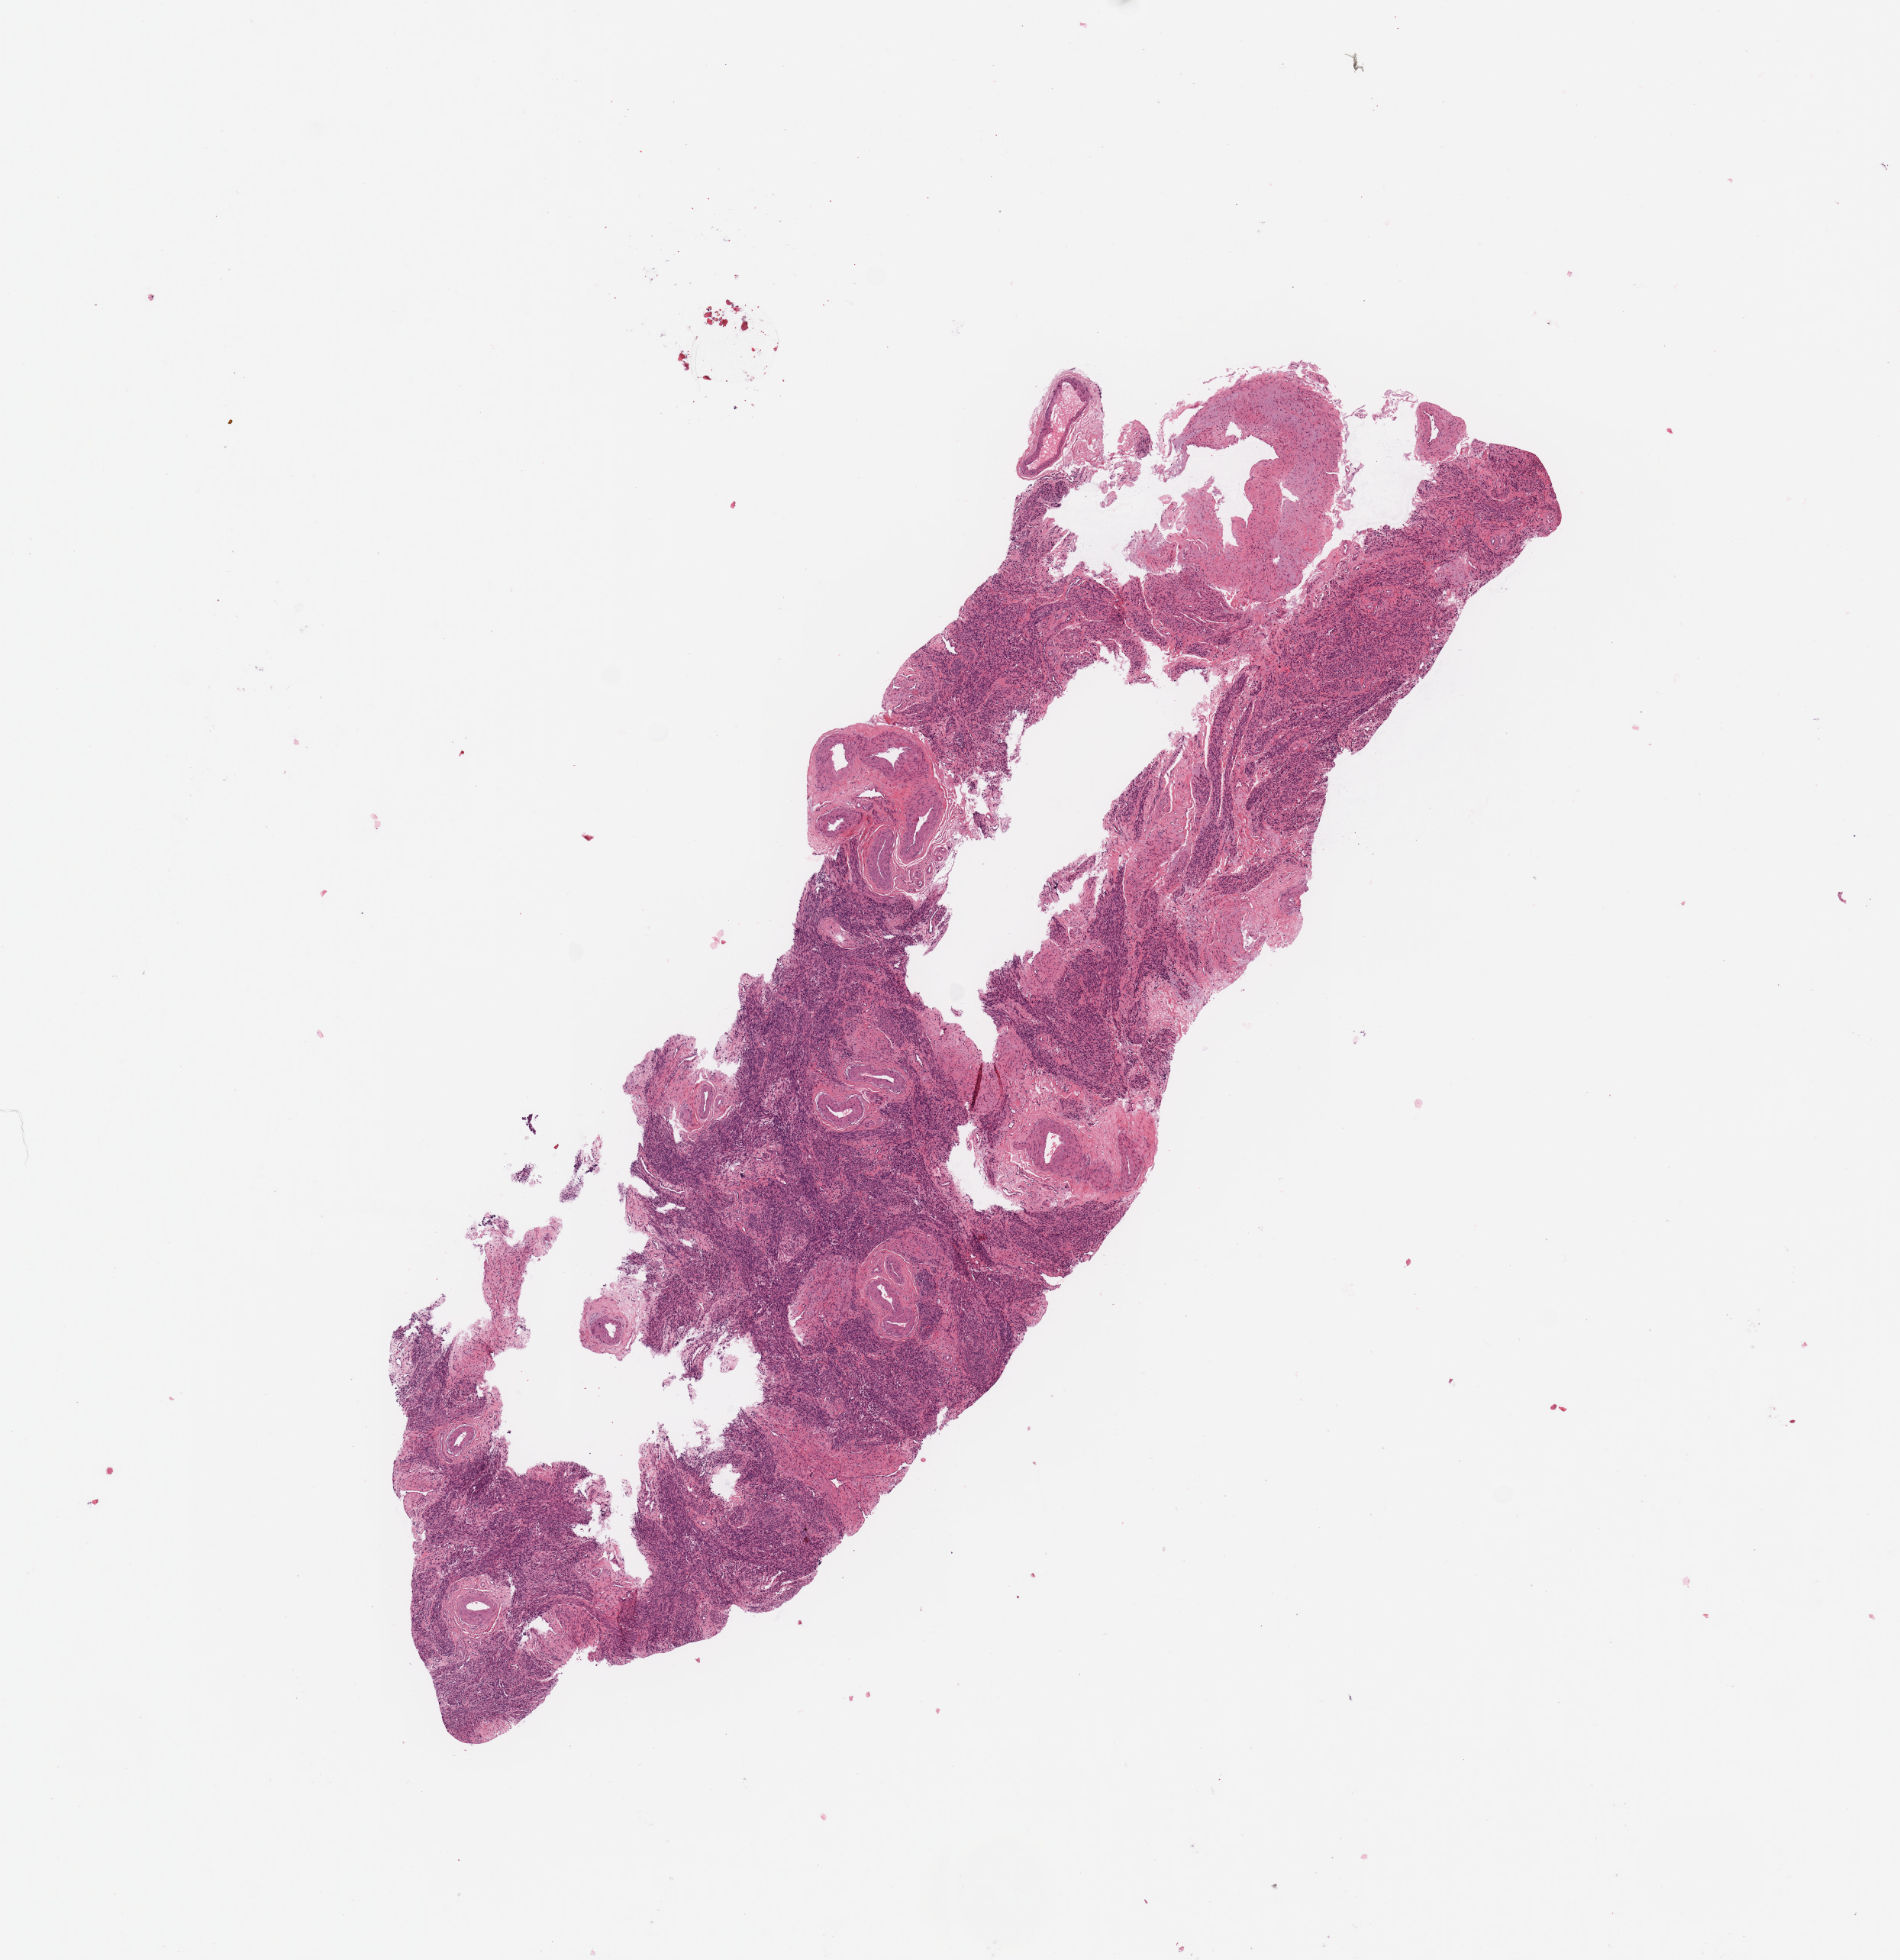
Whole-slide histology image, H&E — low-resolution overview of the scanned area, about 9.8 x 10.2 mm, normal (non-tumour) tissue sample, sampled site: uterus. 73-year-old female patient.
This section: normal (non-tumour) tissue from the same patient. Patient diagnosis: Endometrioid adenocarcinoma, NOS.